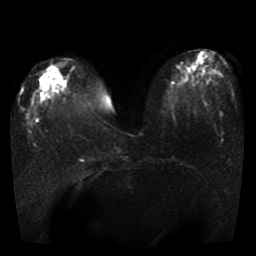
Breast MRI, one axial slice. Diffusion-weighted series; image 2 of 4 stored at this slice position (different b-values; order by instance number). 1.5 T. 5 mm slice thickness. 256 × 256 image matrix. Female patient.
Annotated regions visible in this slice (expert manual segmentation):
- tumour on diffusion-weighted imaging: bounding box (x1, y1, x2, y2) in pixels: (40, 77, 51, 93)